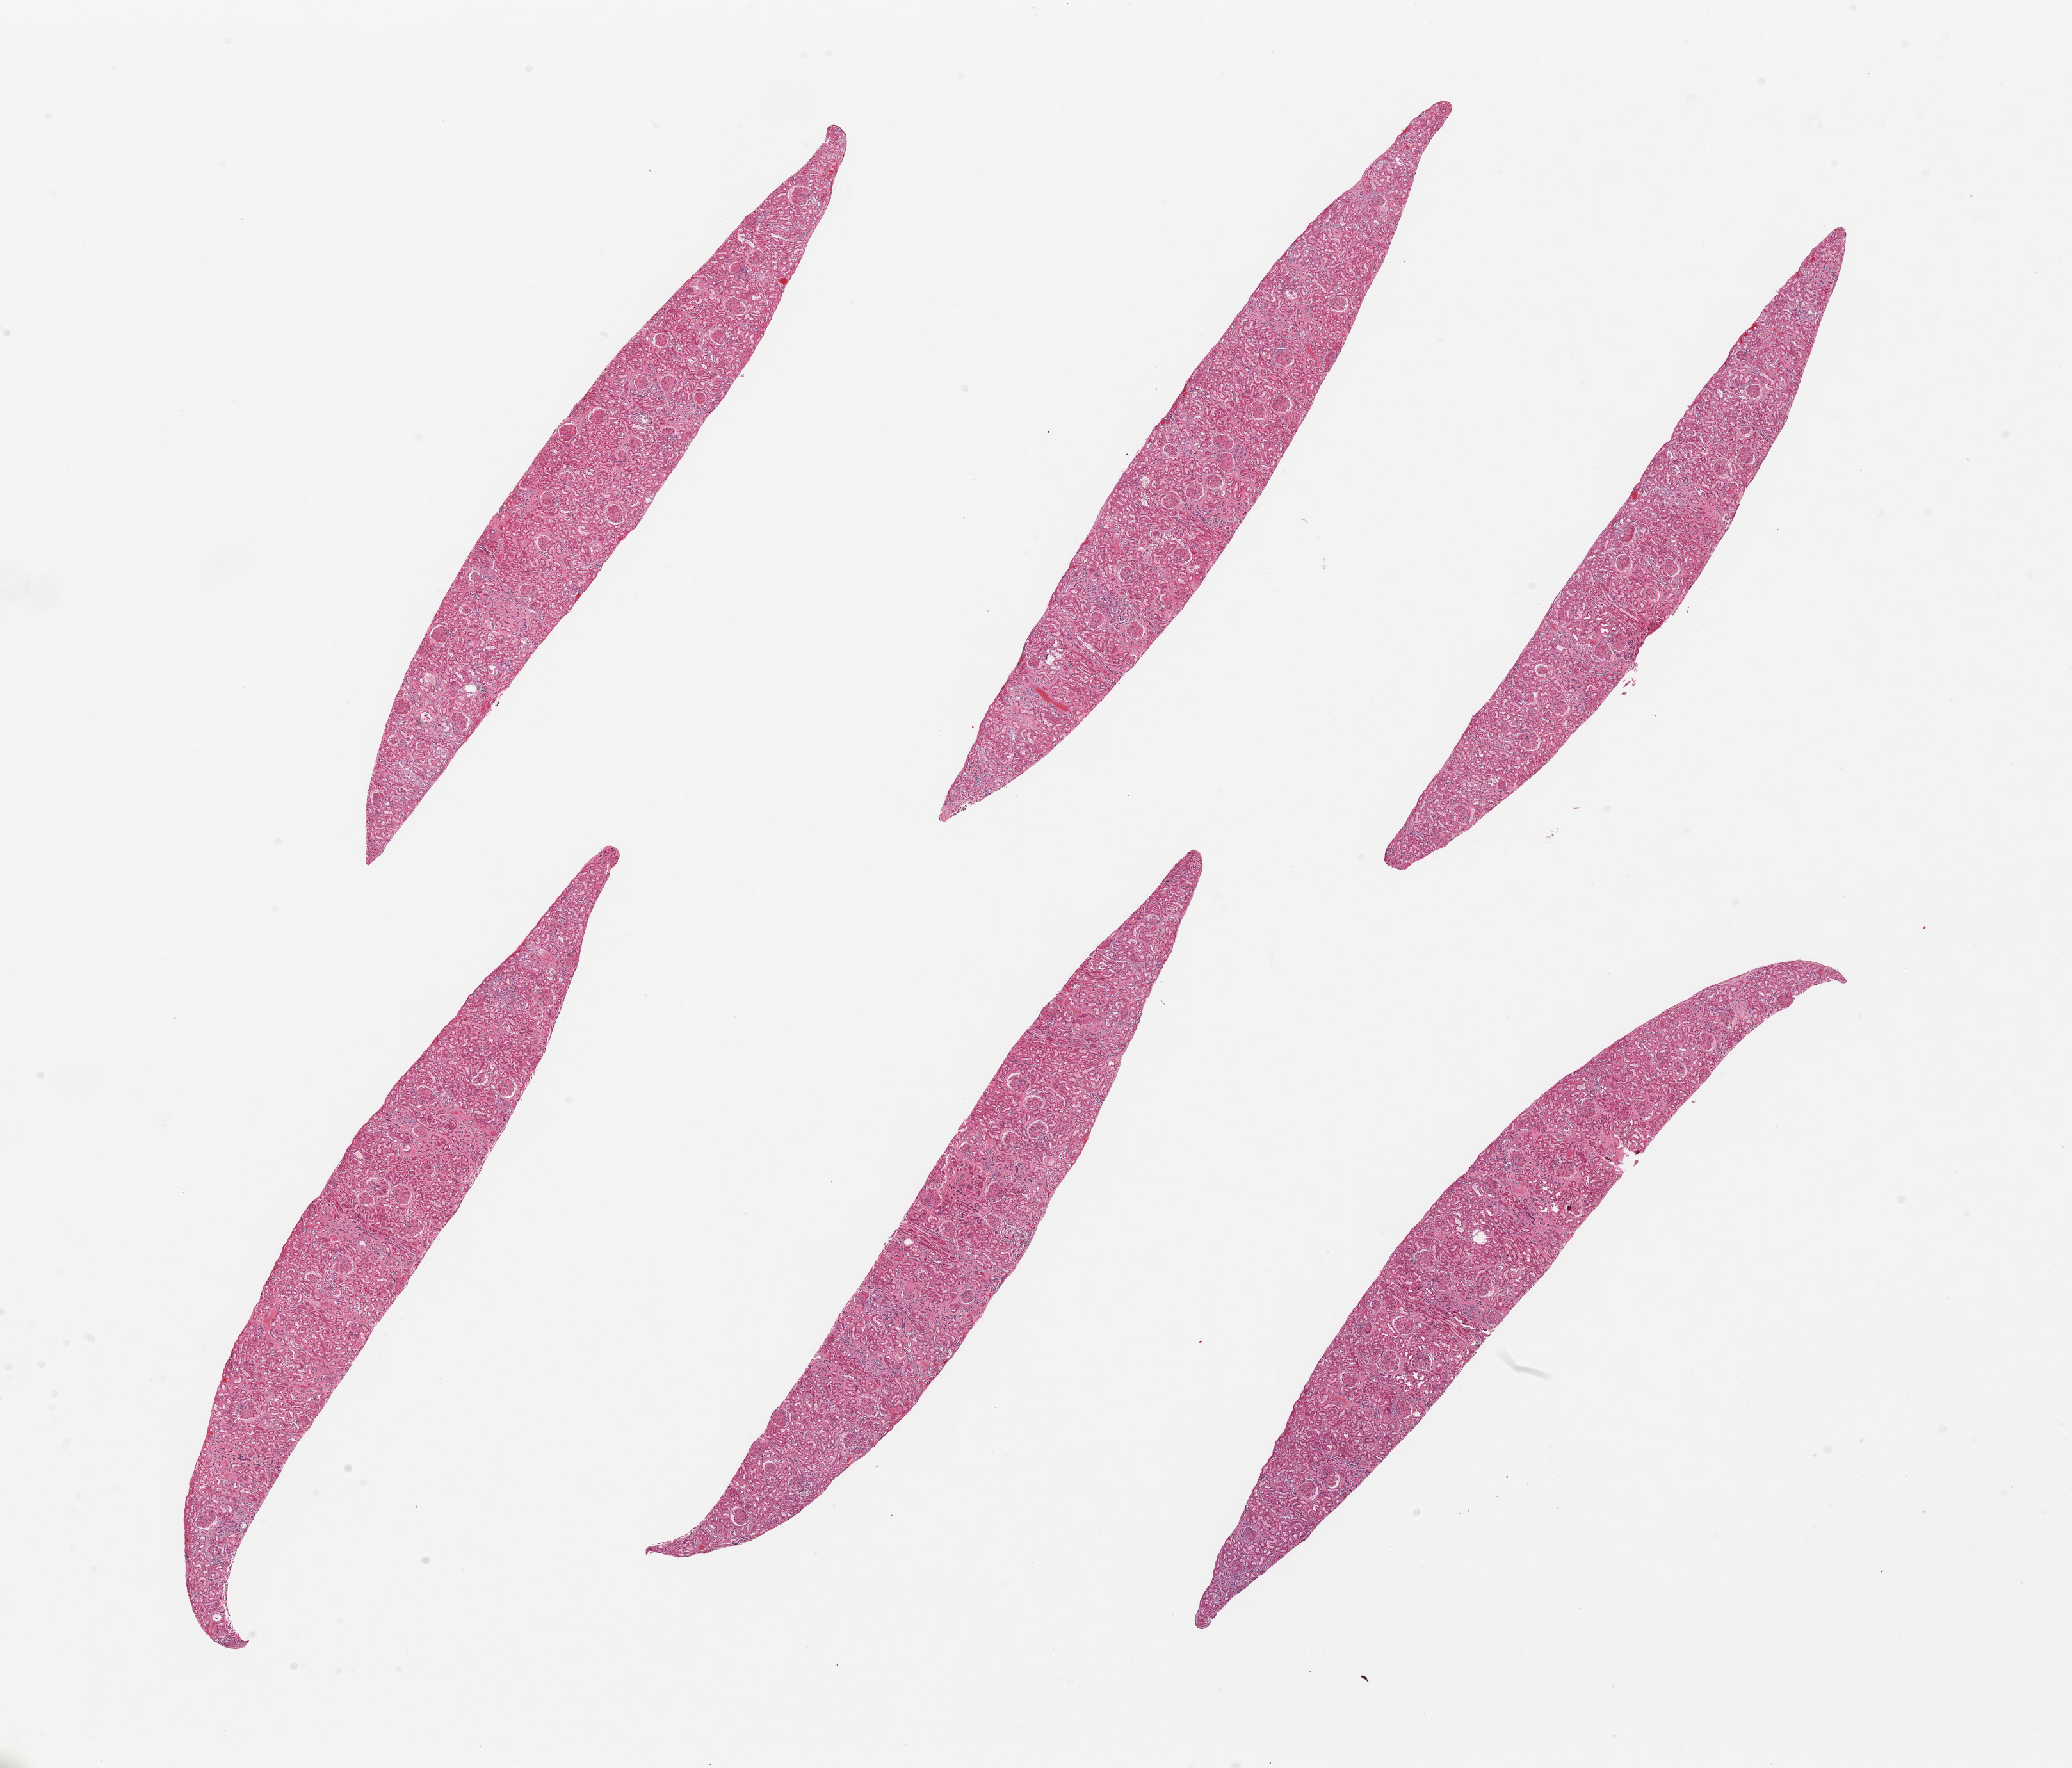
Digitized H&E-stained section — whole scanned area (about 25.6 x 21.8 mm, acquisition: 20x scan) shown as a low-resolution overview, PAXgene-fixed, paraffin-embedded tissue, target tissue: renal cortex, donor tissue sample. Male donor.
Pathologist's review note for this sample: 6 pieces; scattered mild focal interstitial fibrosis; no sign of acute or chronic disease.